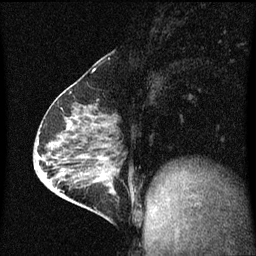
Breast MRI (dynamic contrast-enhanced), one sagittal slice; slice 26 of 60 in the series (ordered by position); dynamic contrast-enhanced series, image 2 of 3 at this slice position (ordered by acquisition); 1.5 T; TE 4.2 ms, TR 8 ms; 2 mm slice thickness; 256 × 256 image matrix, field of view 200 × 200 mm. Patient: female, 64 years.
Annotated regions visible in this slice (semi-automatically segmented with operator editing):
- analysis volume of interest (the breast-tissue region the enhancement analysis was run in; not a lesion): box from (x=87, y=176) to (x=120, y=217) px
- tumour enhancement mask (voxels above the 70 % enhancement threshold inside the analysis volume of interest): (x=93, y=180)–(x=113, y=193)